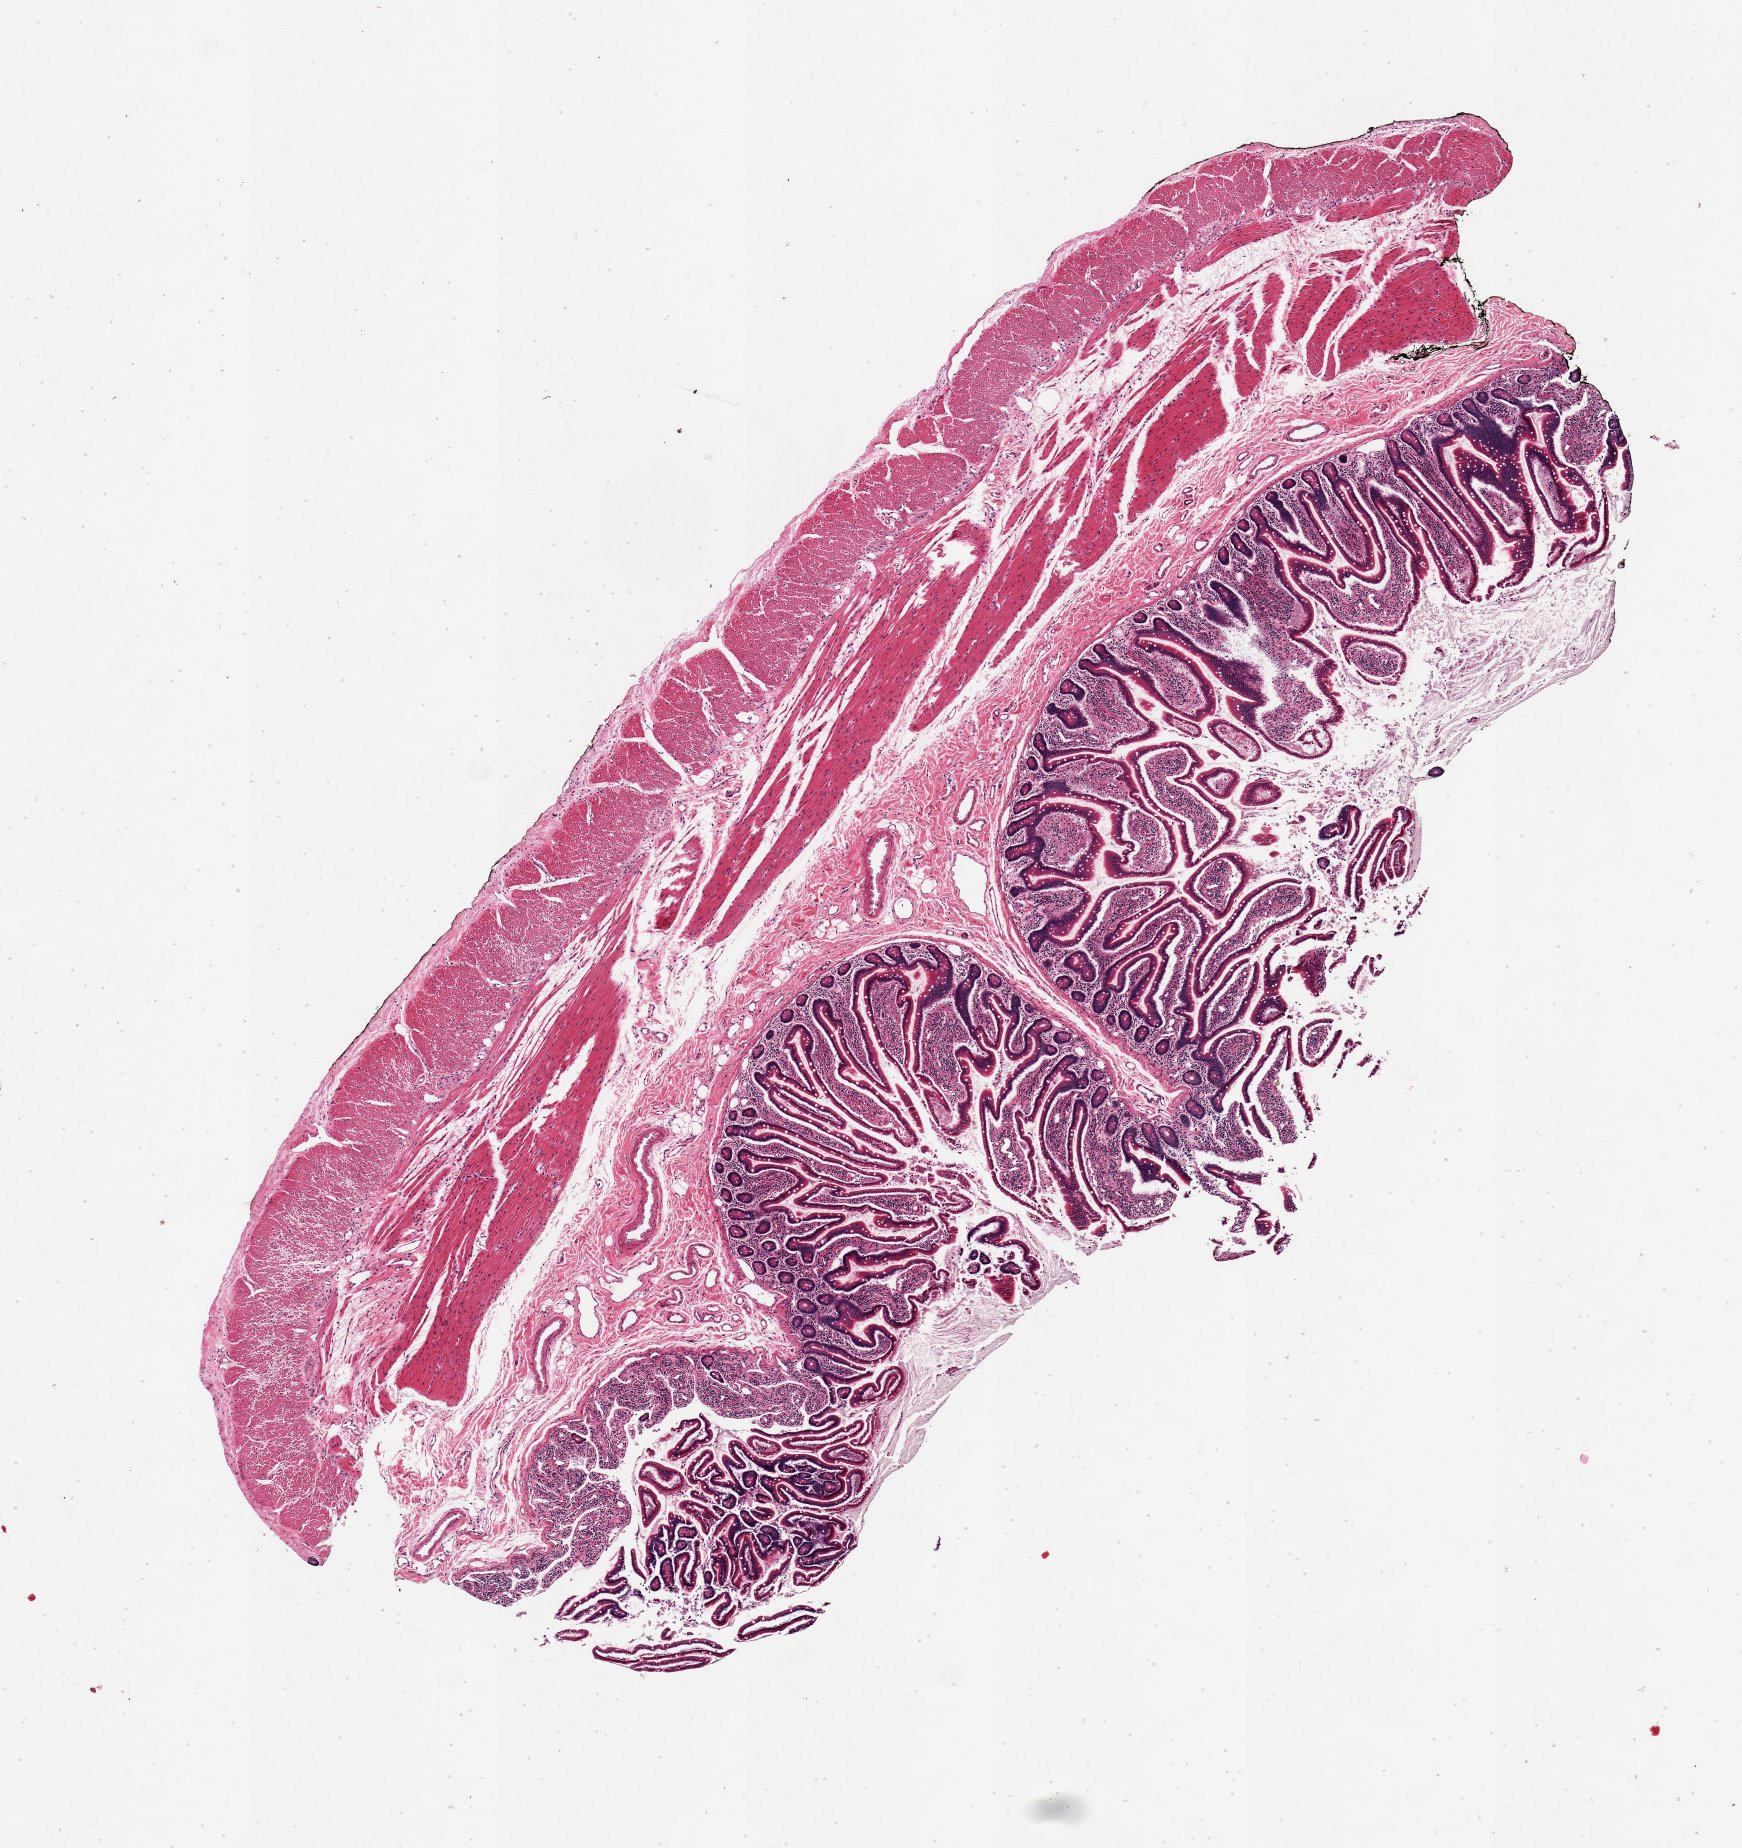
Digitized H&E-stained section, whole scanned area (about 6.9 x 7.3 mm) shown as a low-resolution overview, PAXgene-fixed, paraffin-embedded tissue, section of transverse colon (target tissue), tissue donor sample.
* review note (as recorded): 1 piece. 7x3.5mm; small intestine not colon